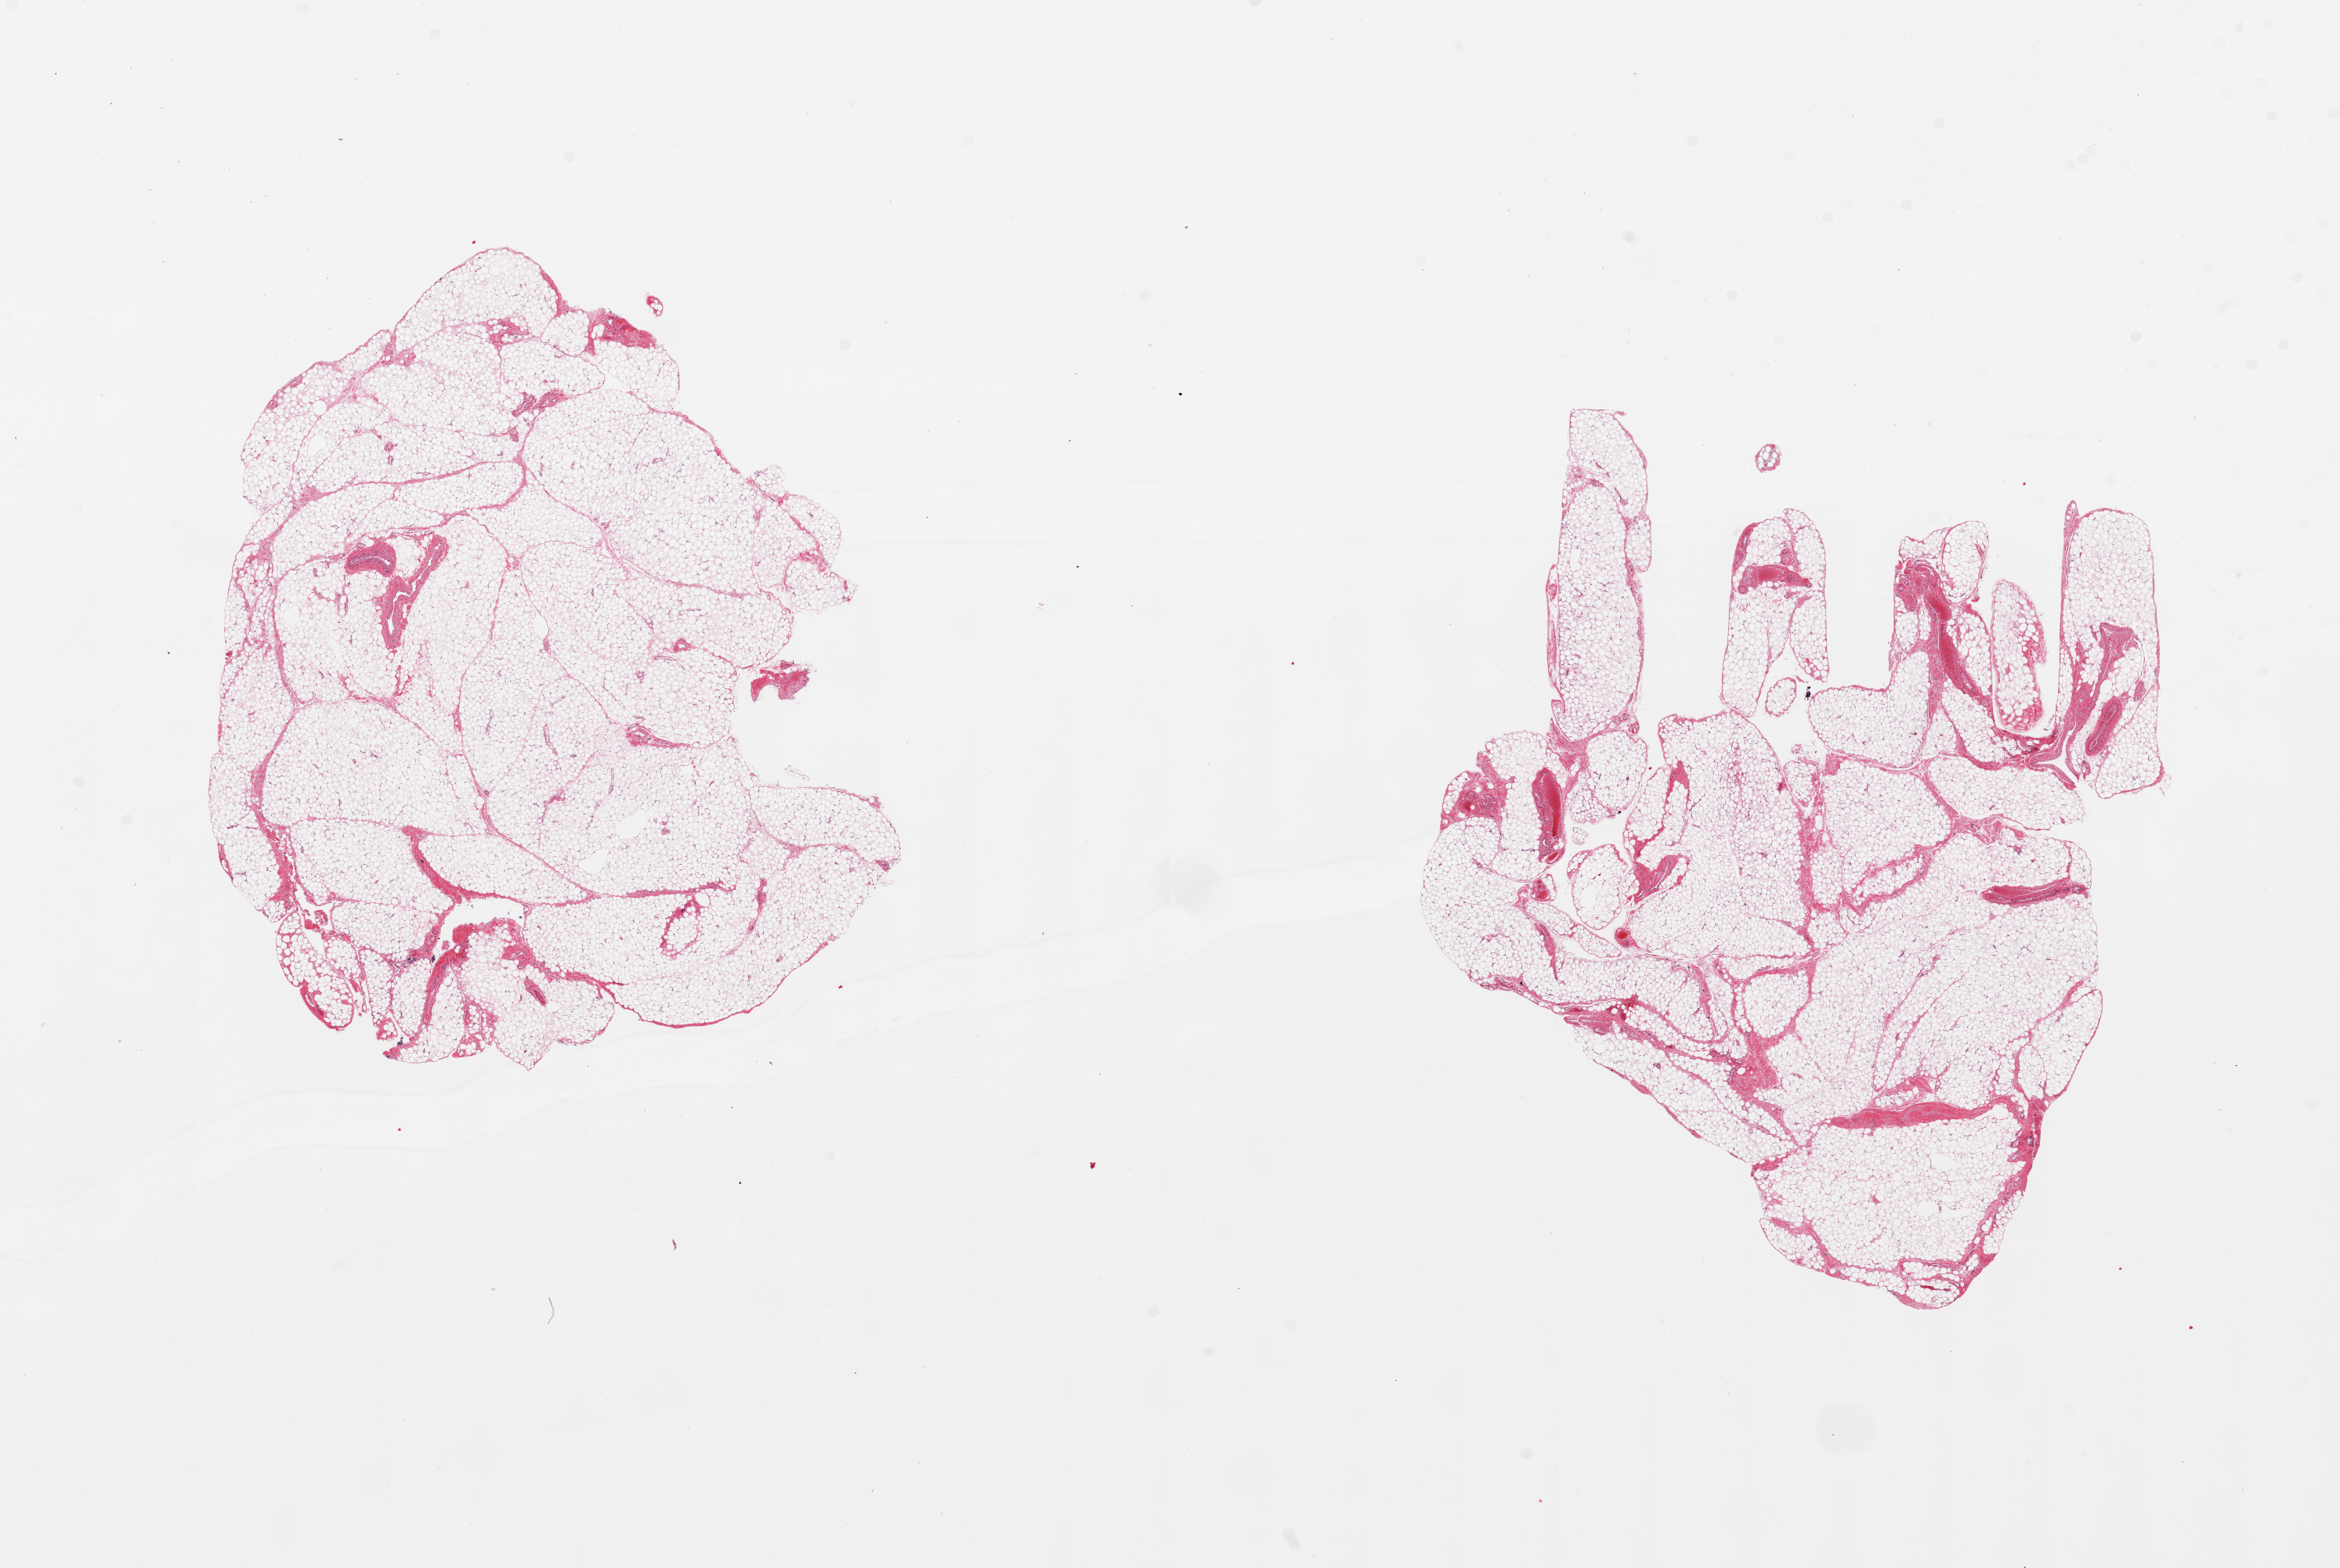
Hematoxylin and eosin (H&E) whole-slide image, shown as a low-resolution overview of the whole scanned area (about 23.6 x 15.8 mm). PAXgene-fixed, paraffin-embedded tissue. Section of omentum (target tissue). Donor tissue sample. Female donor.
Review note (as recorded): 2 pieces, minimal fascia/fbirous tissue.